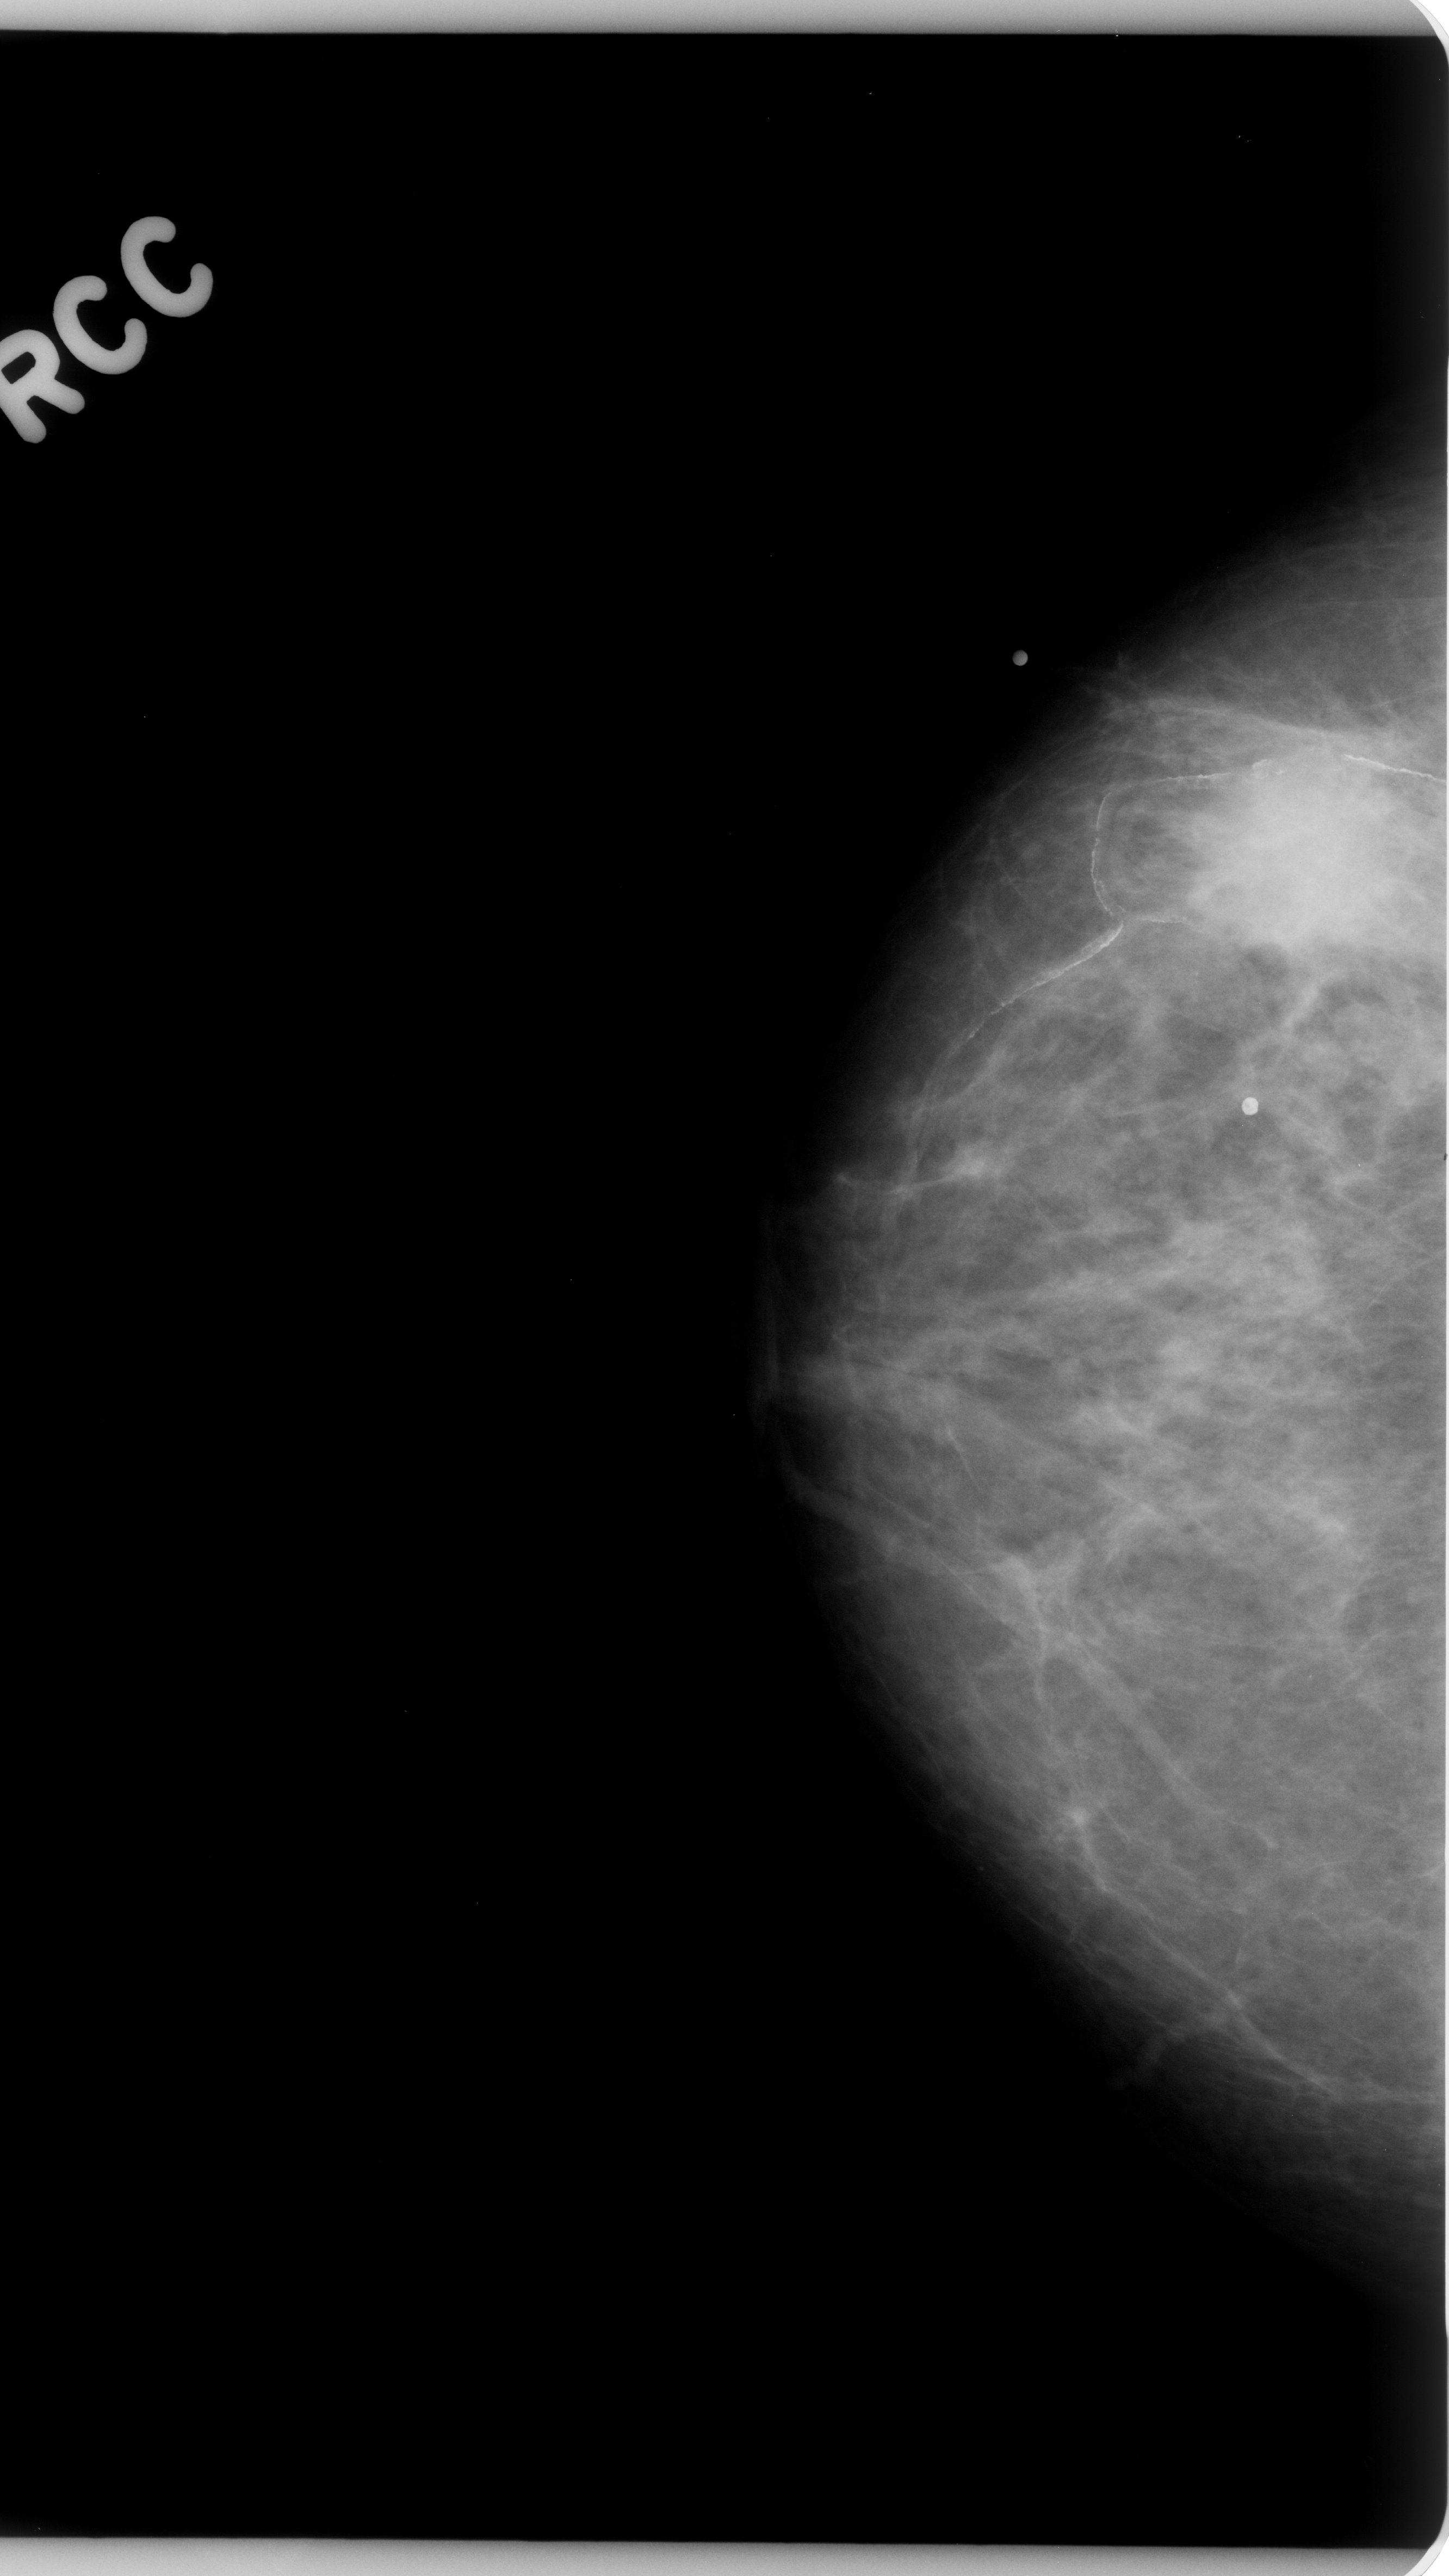
Mammogram (digitized film); right breast; craniocaudal (CC) view; BI-RADS breast density category 2 (scale 1–4).
Abnormality record for this image: mass, shape round, margins ill defined; BI-RADS assessment category 5; pathology (as recorded): malignant.